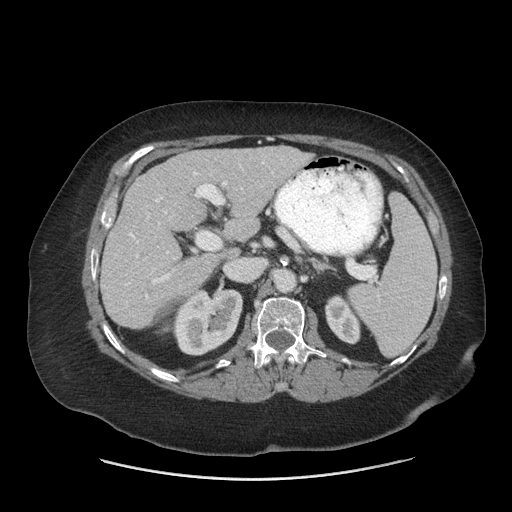
Contrast-enhanced abdominal CT (liver protocol), one axial slice. Slice 35 of 69 in the series (ordered by position). Reconstruction kernel STANDARD. 140 kVp. Soft-tissue window (W 400 / L 40 HU). 2.5 mm slice thickness. 512 × 512 image matrix. From the clinical record (not read from this slice): diagnosis: hepatocellular carcinoma (patient treated with transarterial chemoembolisation; whether this scan precedes or follows treatment is not stated here); TNM stage (as recorded): Stage-IIIB; Child-Pugh class: A; tumour differentiation: moderately differentiated.
Outlined on this slice (semi-automatically segmented with operator editing):
- liver parenchyma outside the tumour (the mass and vessels are separate outlines, so this box may not span the whole liver): bounding box [x1, y1, x2, y2] px = [100, 146, 312, 328]
- liver vessels: [126, 161, 274, 299]